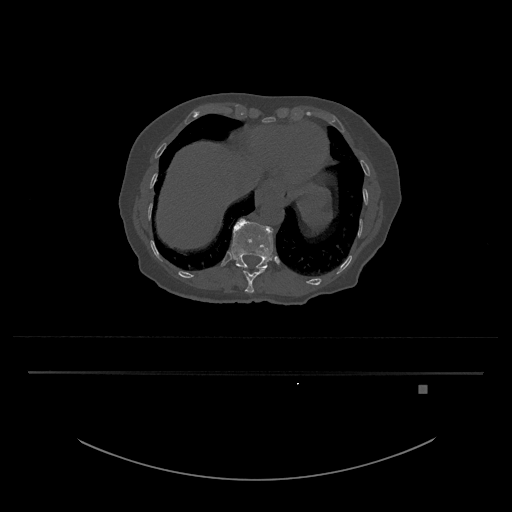
CT including the spine, one axial slice; slice 636 of 797 in the series (ordered by position); reconstruction kernel Br40s/3; 120 kVp; bone window (W 1800 / L 400 HU); 512 × 512 image matrix, field of view 500 × 500 mm. Female patient, age 57 years. From the clinical record (not read from this slice): primary cancer: cervical.
Annotated regions visible in this slice (semi-automatic segmentation, software-assisted and operator-edited):
- T11 vertebra: bounding box [x1, y1, x2, y2] px = [238, 266, 266, 293]
- T12 vertebra: [231, 218, 273, 269]